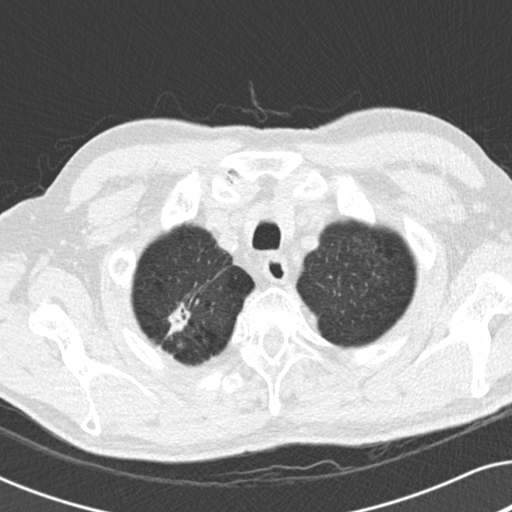
Low-dose screening chest CT, one axial slice; slice 171 of 191 in the series (ordered by position); reconstruction kernel B30f; 120 kVp; lung window (W 1500 / L -600 HU); 512 × 512 image matrix.
Outlined on this slice (expert manual segmentation):
- lesion 2 (nodule, lower lobe of right lung): bounding box [x1, y1, x2, y2] px = [167, 305, 191, 337]